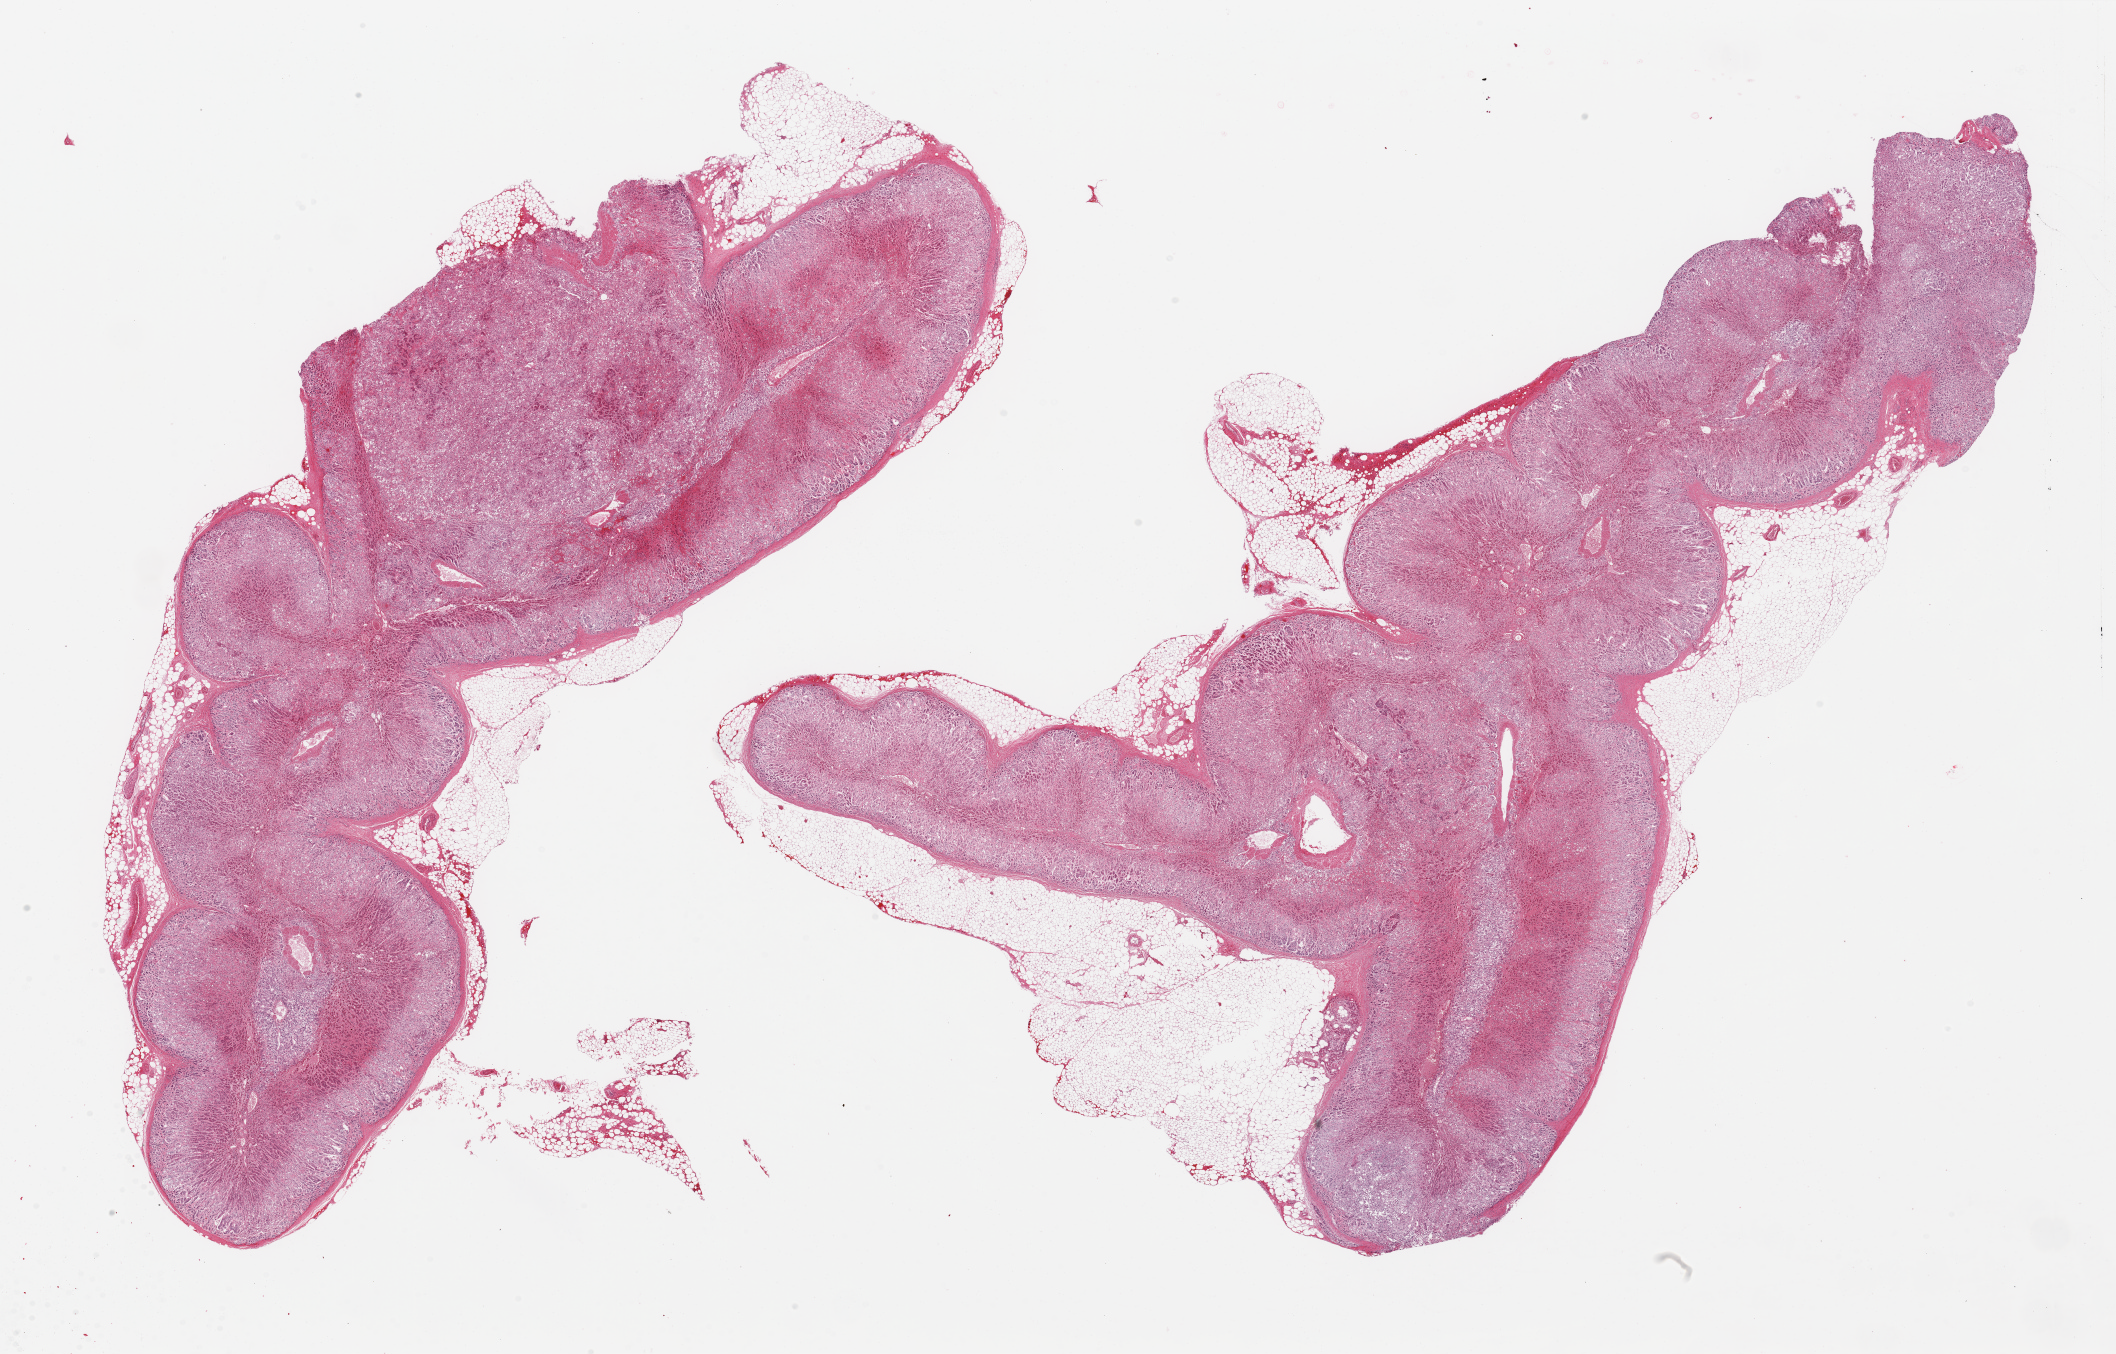
Digitized hematoxylin and eosin (H&E)-stained section, brightfield, low-resolution overview of the scanned area, about 33.5 x 21.4 mm; PAXgene-fixed paraffin-embedded (PFPE) section; target tissue: adrenal gland; tissue donor sample. Donor sex: female.
Reviewer comment on this tissue sample: 2 aliquots ~ 20x7mm (nearly full sections), all cortex but generally badly autolyzed.